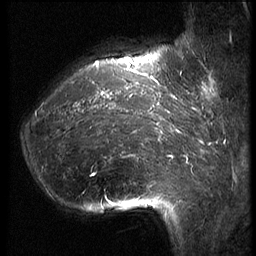
Breast MRI (dynamic contrast-enhanced), one sagittal slice. Slice 14 of 62 in the series (ordered by position). 3 images stored at this slice position (order not interpretable as contrast timing). 1.5 T. TE 4.2 ms, TR 9 ms. 256 × 256 image matrix, field of view 180 × 180 mm. Patient: female, 39 years. From the clinical record (not read from this slice): setting: breast cancer imaged before/during neoadjuvant chemotherapy; receptor status: HER2-positive.
Outlined on this slice (semi-automatic segmentation, software-assisted and operator-edited):
- analysis volume of interest (the breast-tissue region the enhancement analysis was run in; not a lesion): bounding box <23,64,171,228> (left, top, right, bottom; pixels)
- tumour enhancement mask (voxels above the 140 % enhancement threshold inside the analysis volume of interest): <65,64,169,175>